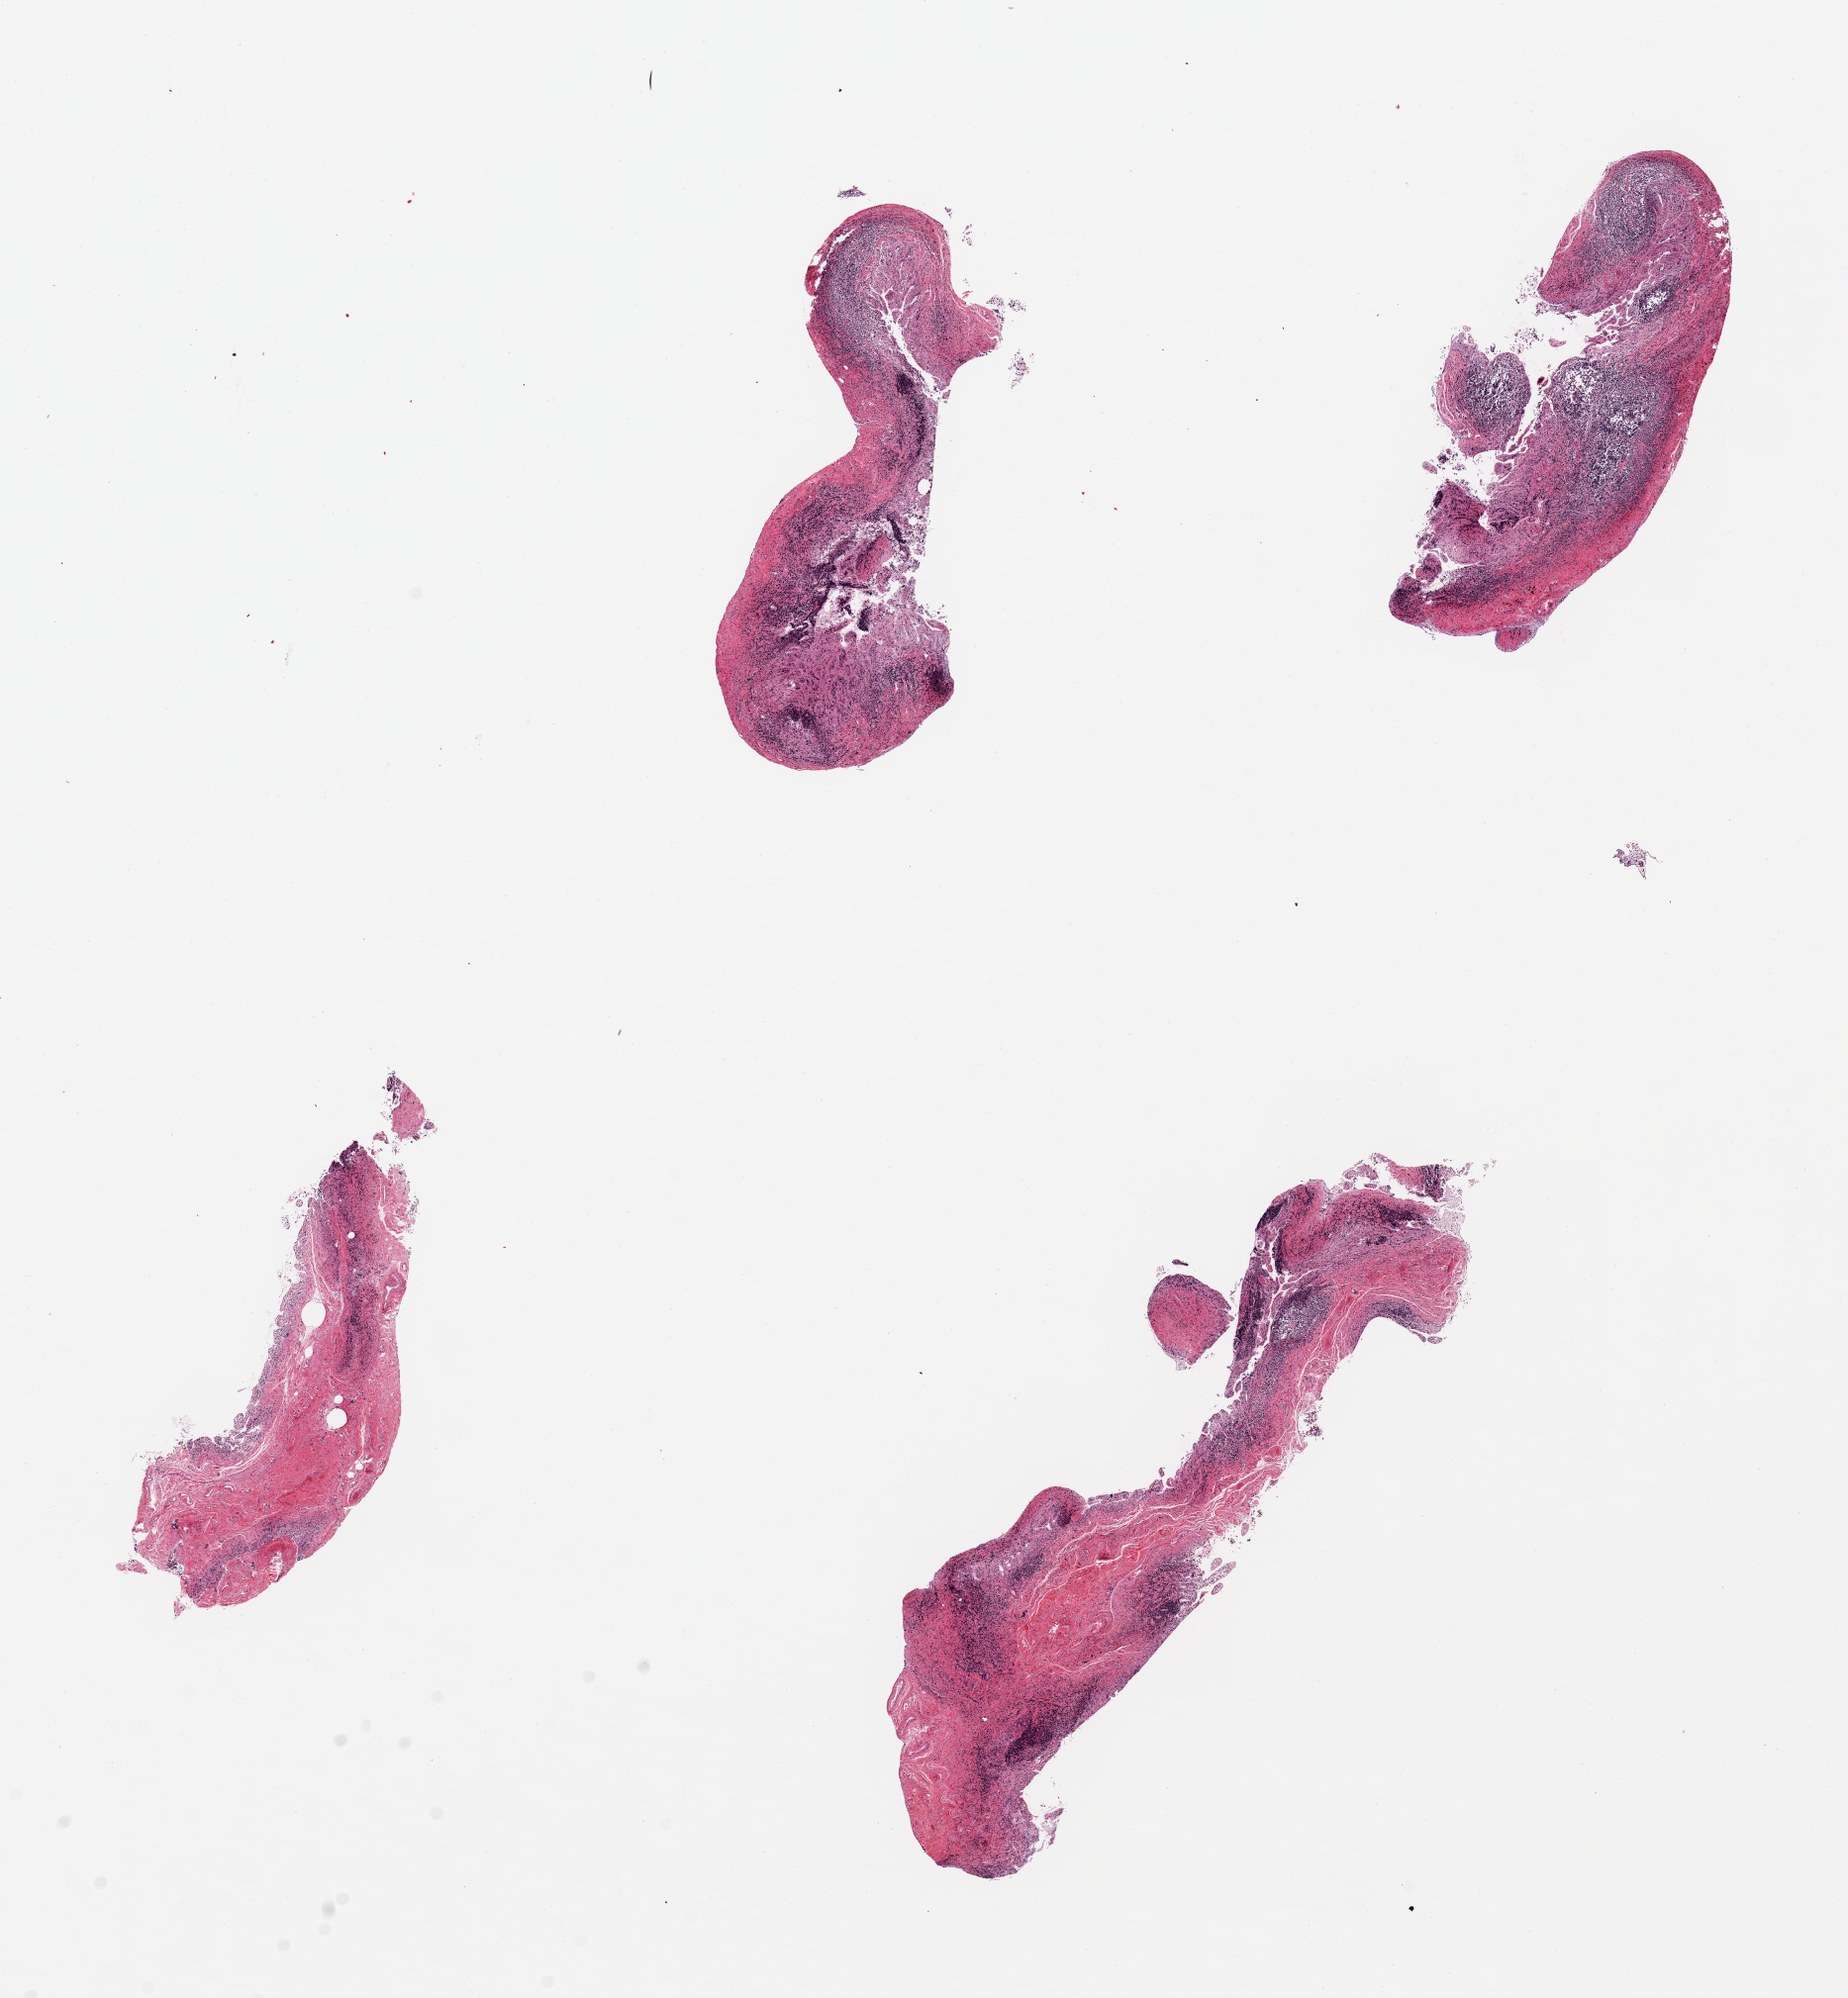
H&E whole-slide image, whole scanned area (about 14.8 x 16.0 mm) shown as a low-resolution overview. PAXgene-fixed, paraffin-embedded tissue. Sampled site (target tissue): ileum. Tissue donor sample. Male donor.
Review note (as recorded): 4 pieces, up to 7x2mm; mucosa=3; lymphoid tissue=2 (autolysis); well dissected for Peyer Patches.